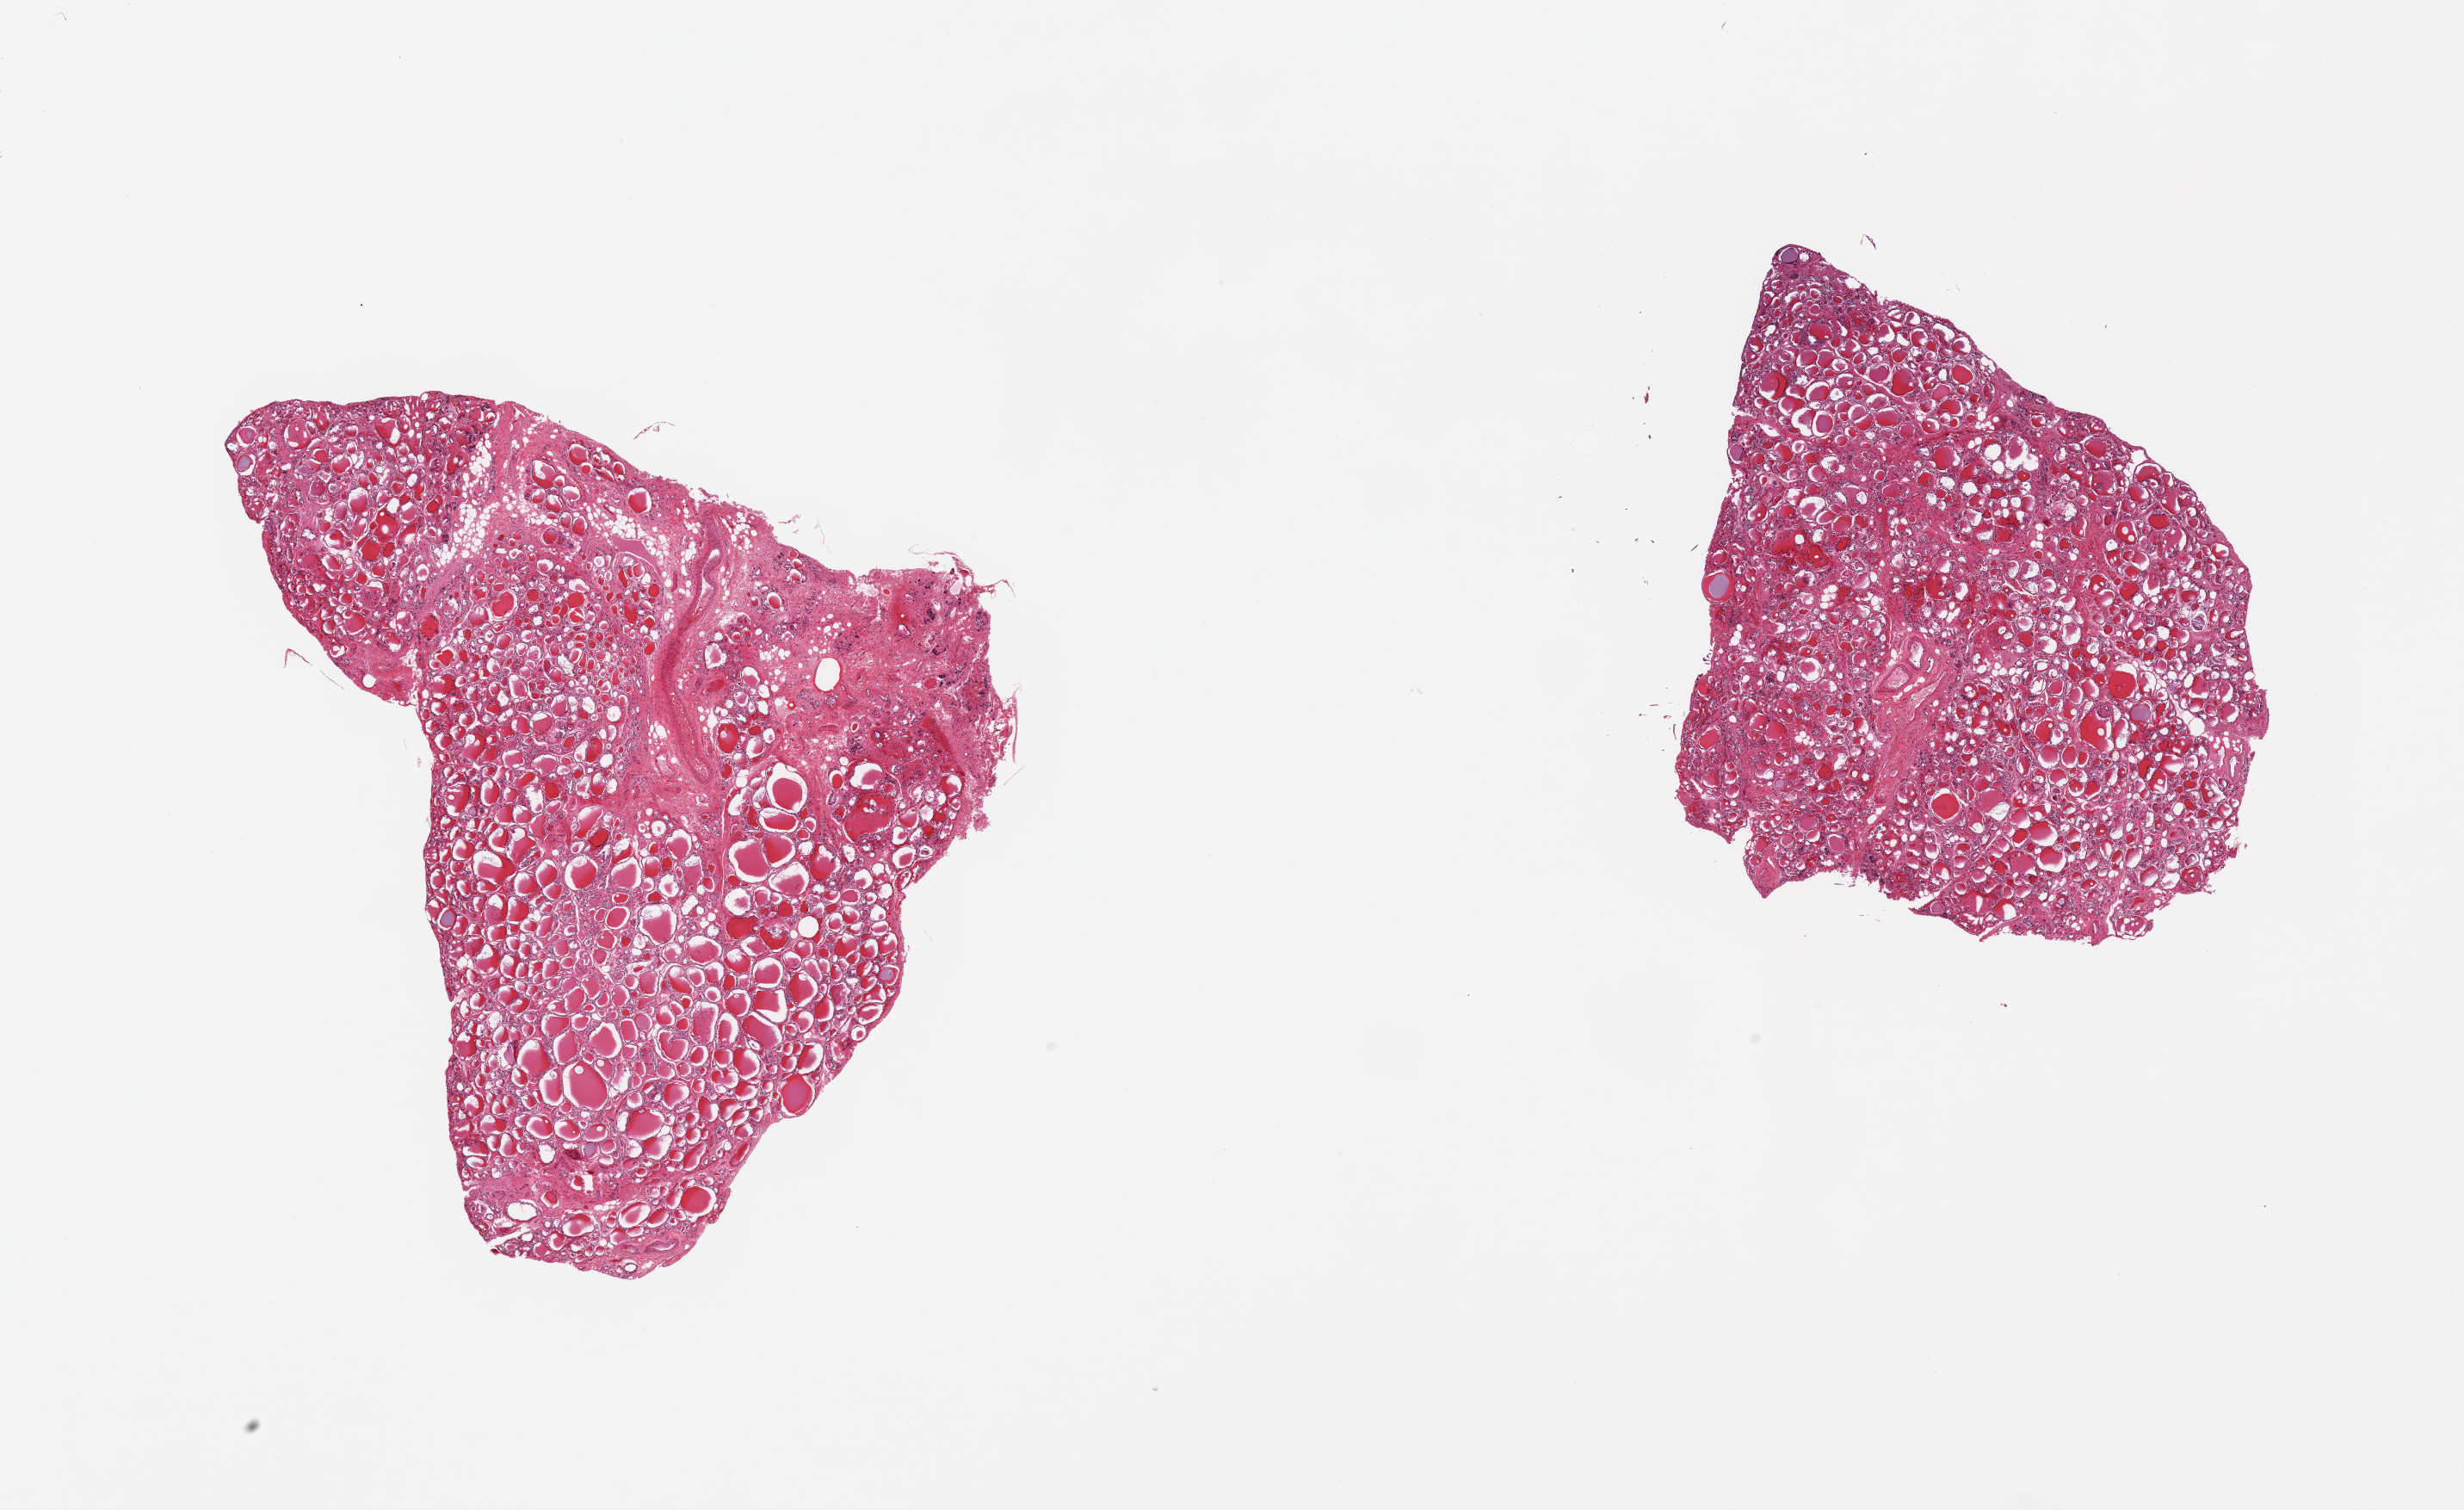
Whole-slide image, haematoxylin and eosin stain, brightfield — whole scanned area (about 22.6 x 13.9 mm, acquisition: 20x scan) shown as a low-resolution overview; PAXgene-fixed paraffin-embedded (PFPE) section; sampled site (target tissue): thyroid; donor tissue sample. Donor: female.
Review note (as recorded): 2 pieces; 1 piece has 10% fibrous content.